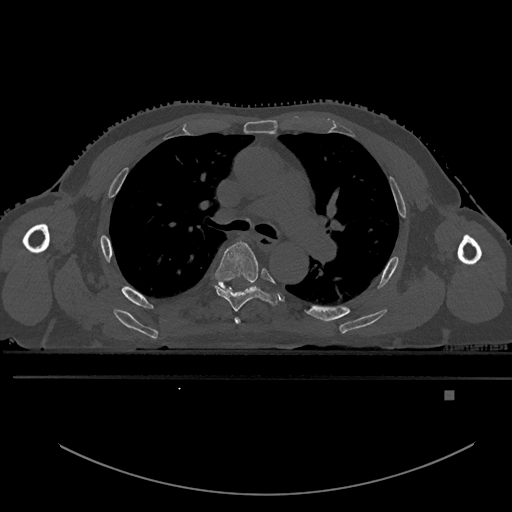
CT including the spine, one axial slice. Position 356 of 969 along the scan axis. Bone window (W 1800 / L 400 HU). 512 × 512 image matrix, field of view 456 × 456 mm. Patient: male, 82 years. Case-level facts recorded for this patient, not image findings: primary cancer: prostate.
Annotated regions visible in this slice (semi-automatically segmented with operator editing):
- T4 vertebra: bounding box (x1, y1, x2, y2) in pixels: (234, 317, 241, 324)
- T5 vertebra: (215, 241, 278, 312)
- T6 vertebra: (216, 284, 244, 292)